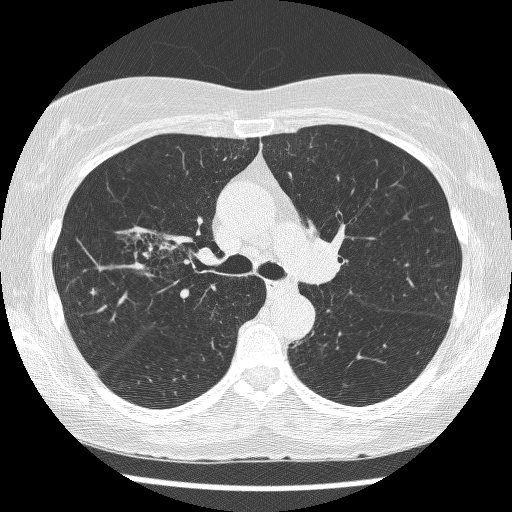
Low-dose screening chest CT, axial slice; baseline screening round; lung window (W 1500 / L -600 HU); 1.25 mm slice thickness; slice 179 of 271 in the series; 512 × 512 image matrix, field of view 316 × 316 mm. Female, age 64 years at enrolment.
- Expert-annotated lung lesion, bounding box (x1, y1, x2, y2) in pixels: (126, 224, 206, 297).
- The screening reader recorded 3 non-calcified nodules or masses ≥4 mm on this exam (right upper lobe, right upper lobe, left lower lobe); which of them this box marks is not recorded.
- Participant outcome: lung cancer diagnosed 735 days after this screen (after the third annual screen) — adenocarcinoma, NOS, right upper lobe, right middle lobe, right hilum, stage IV (AJCC 6th edition), 85 mm at pathology.